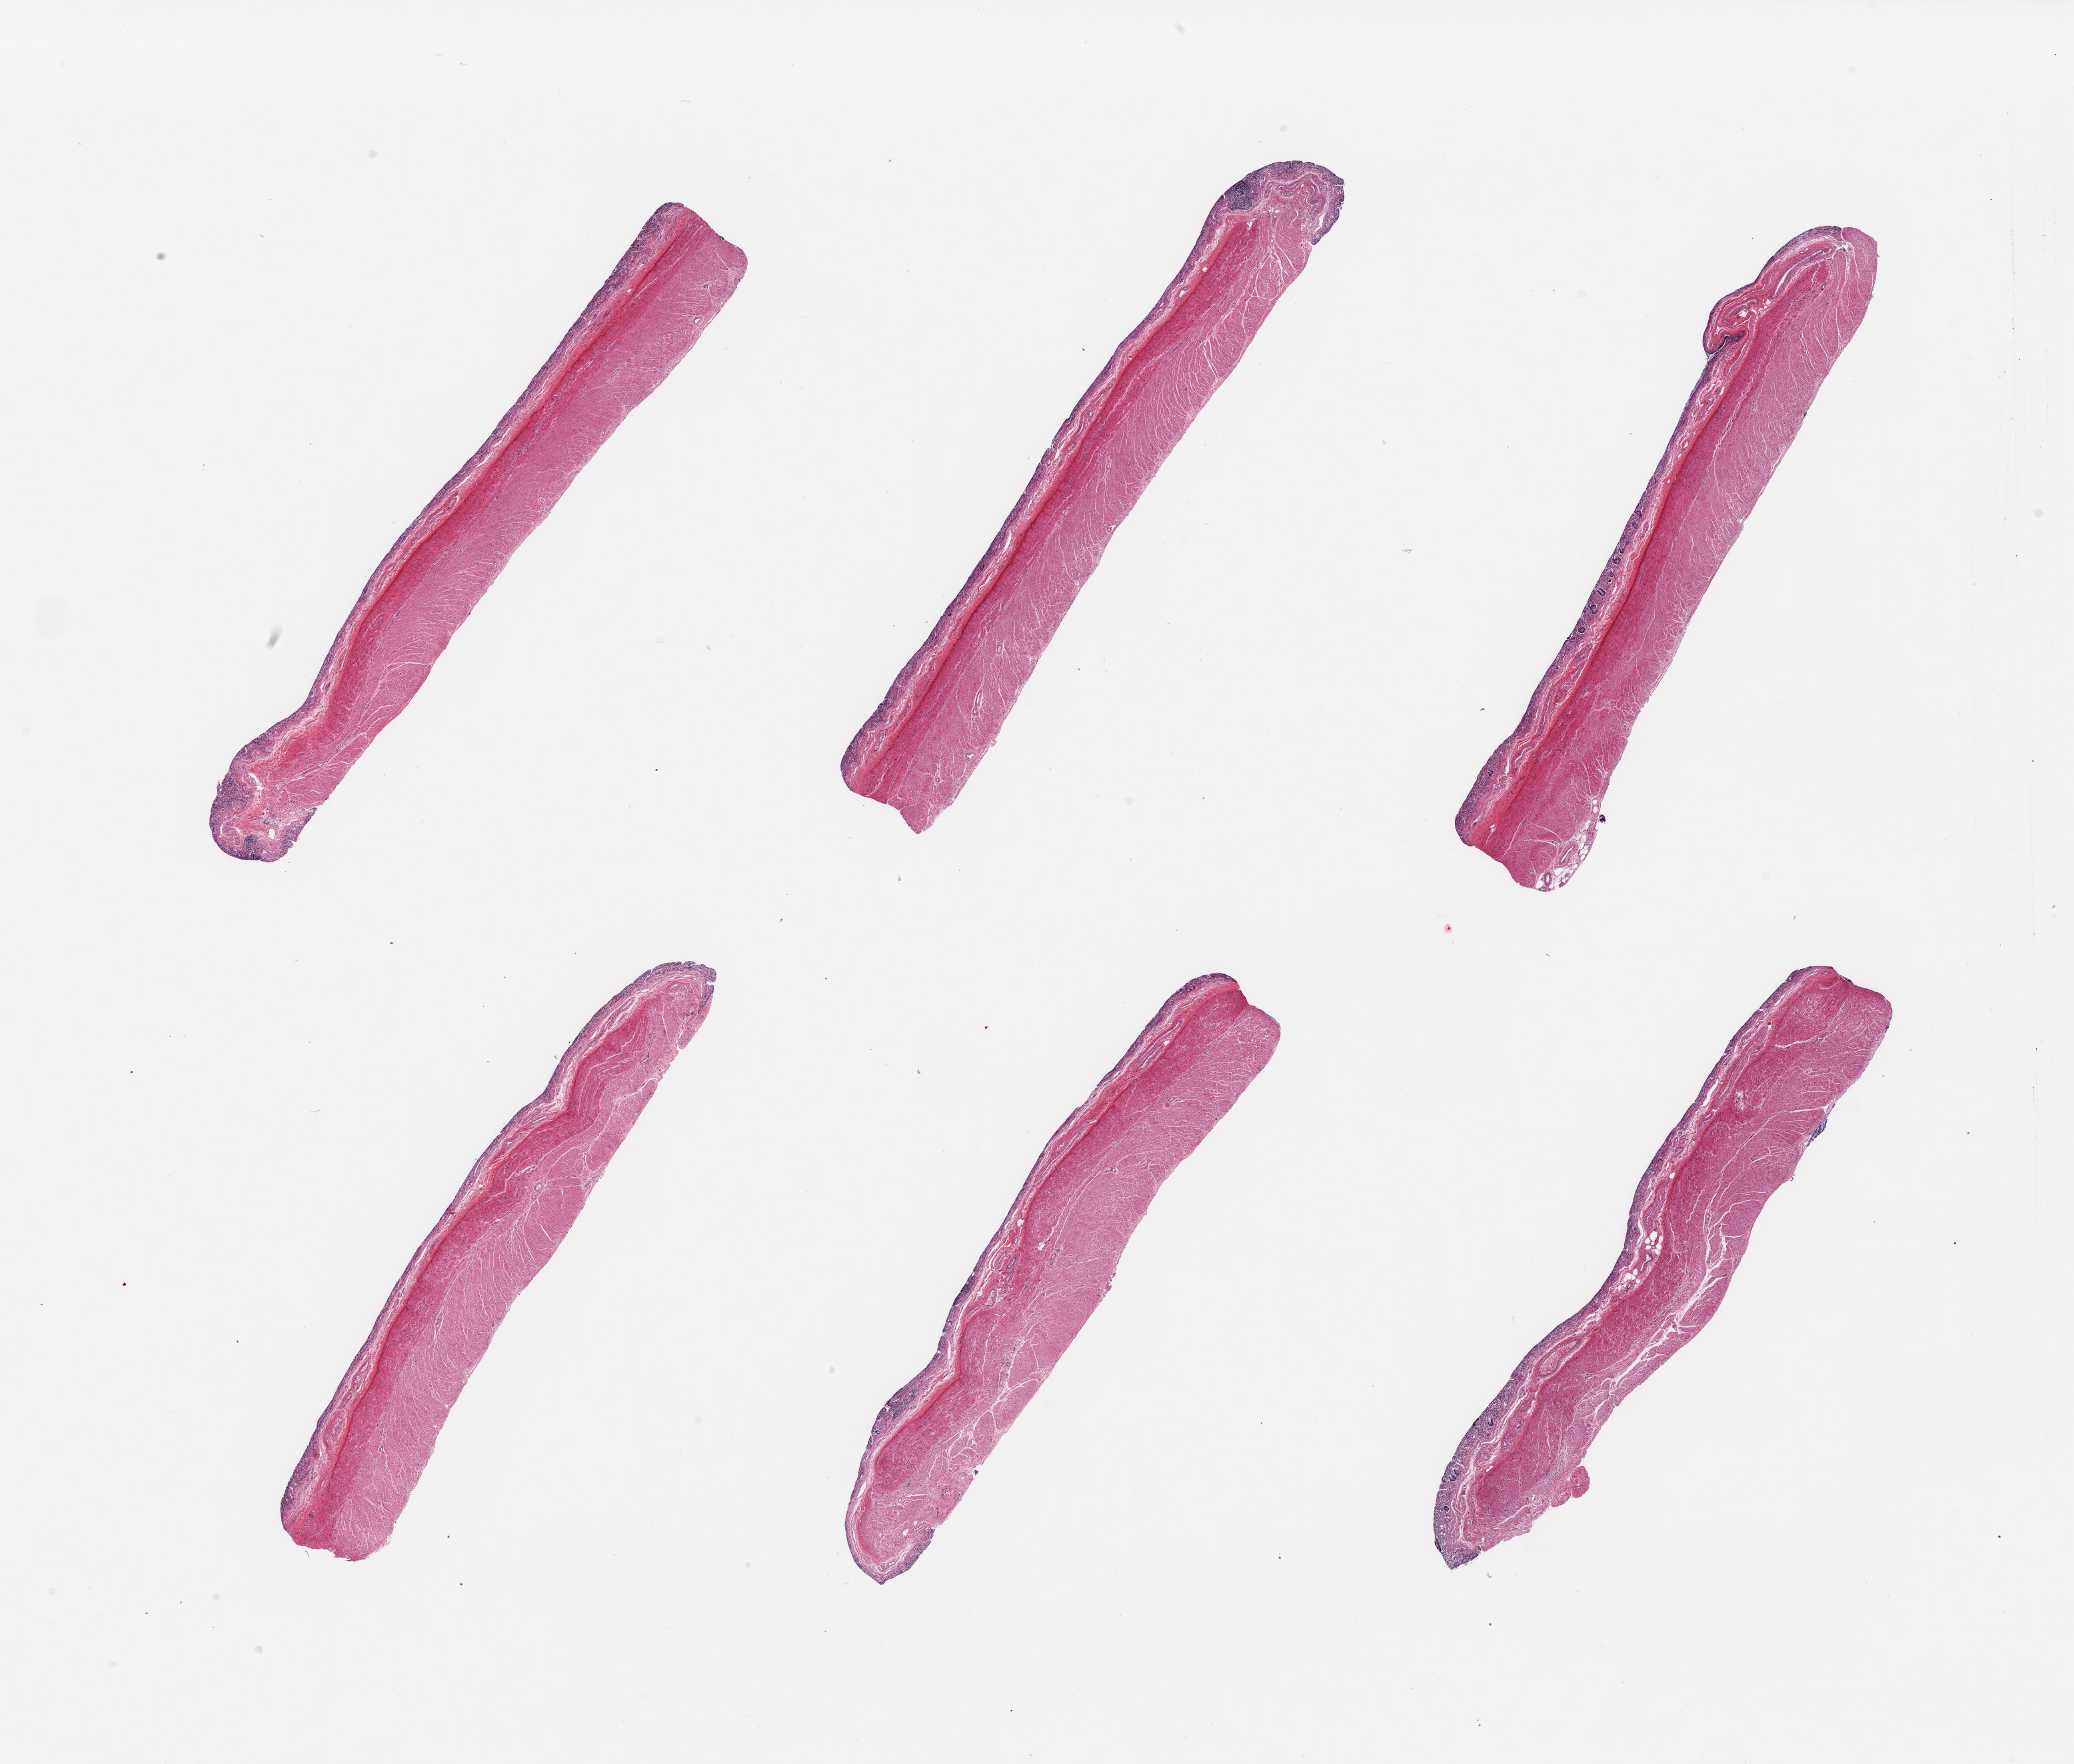
Digitized hematoxylin and eosin (H&E)-stained section, brightfield — a low-resolution overview of the entire scanned area, about 24.6 x 20.9 mm, PAXgene-fixed, paraffin-embedded tissue, sampled site (target tissue): transverse colon, tissue donor sample. Female donor.
- review note (as recorded): 6 pieces; mucosa largely sloughed; muscularis intact